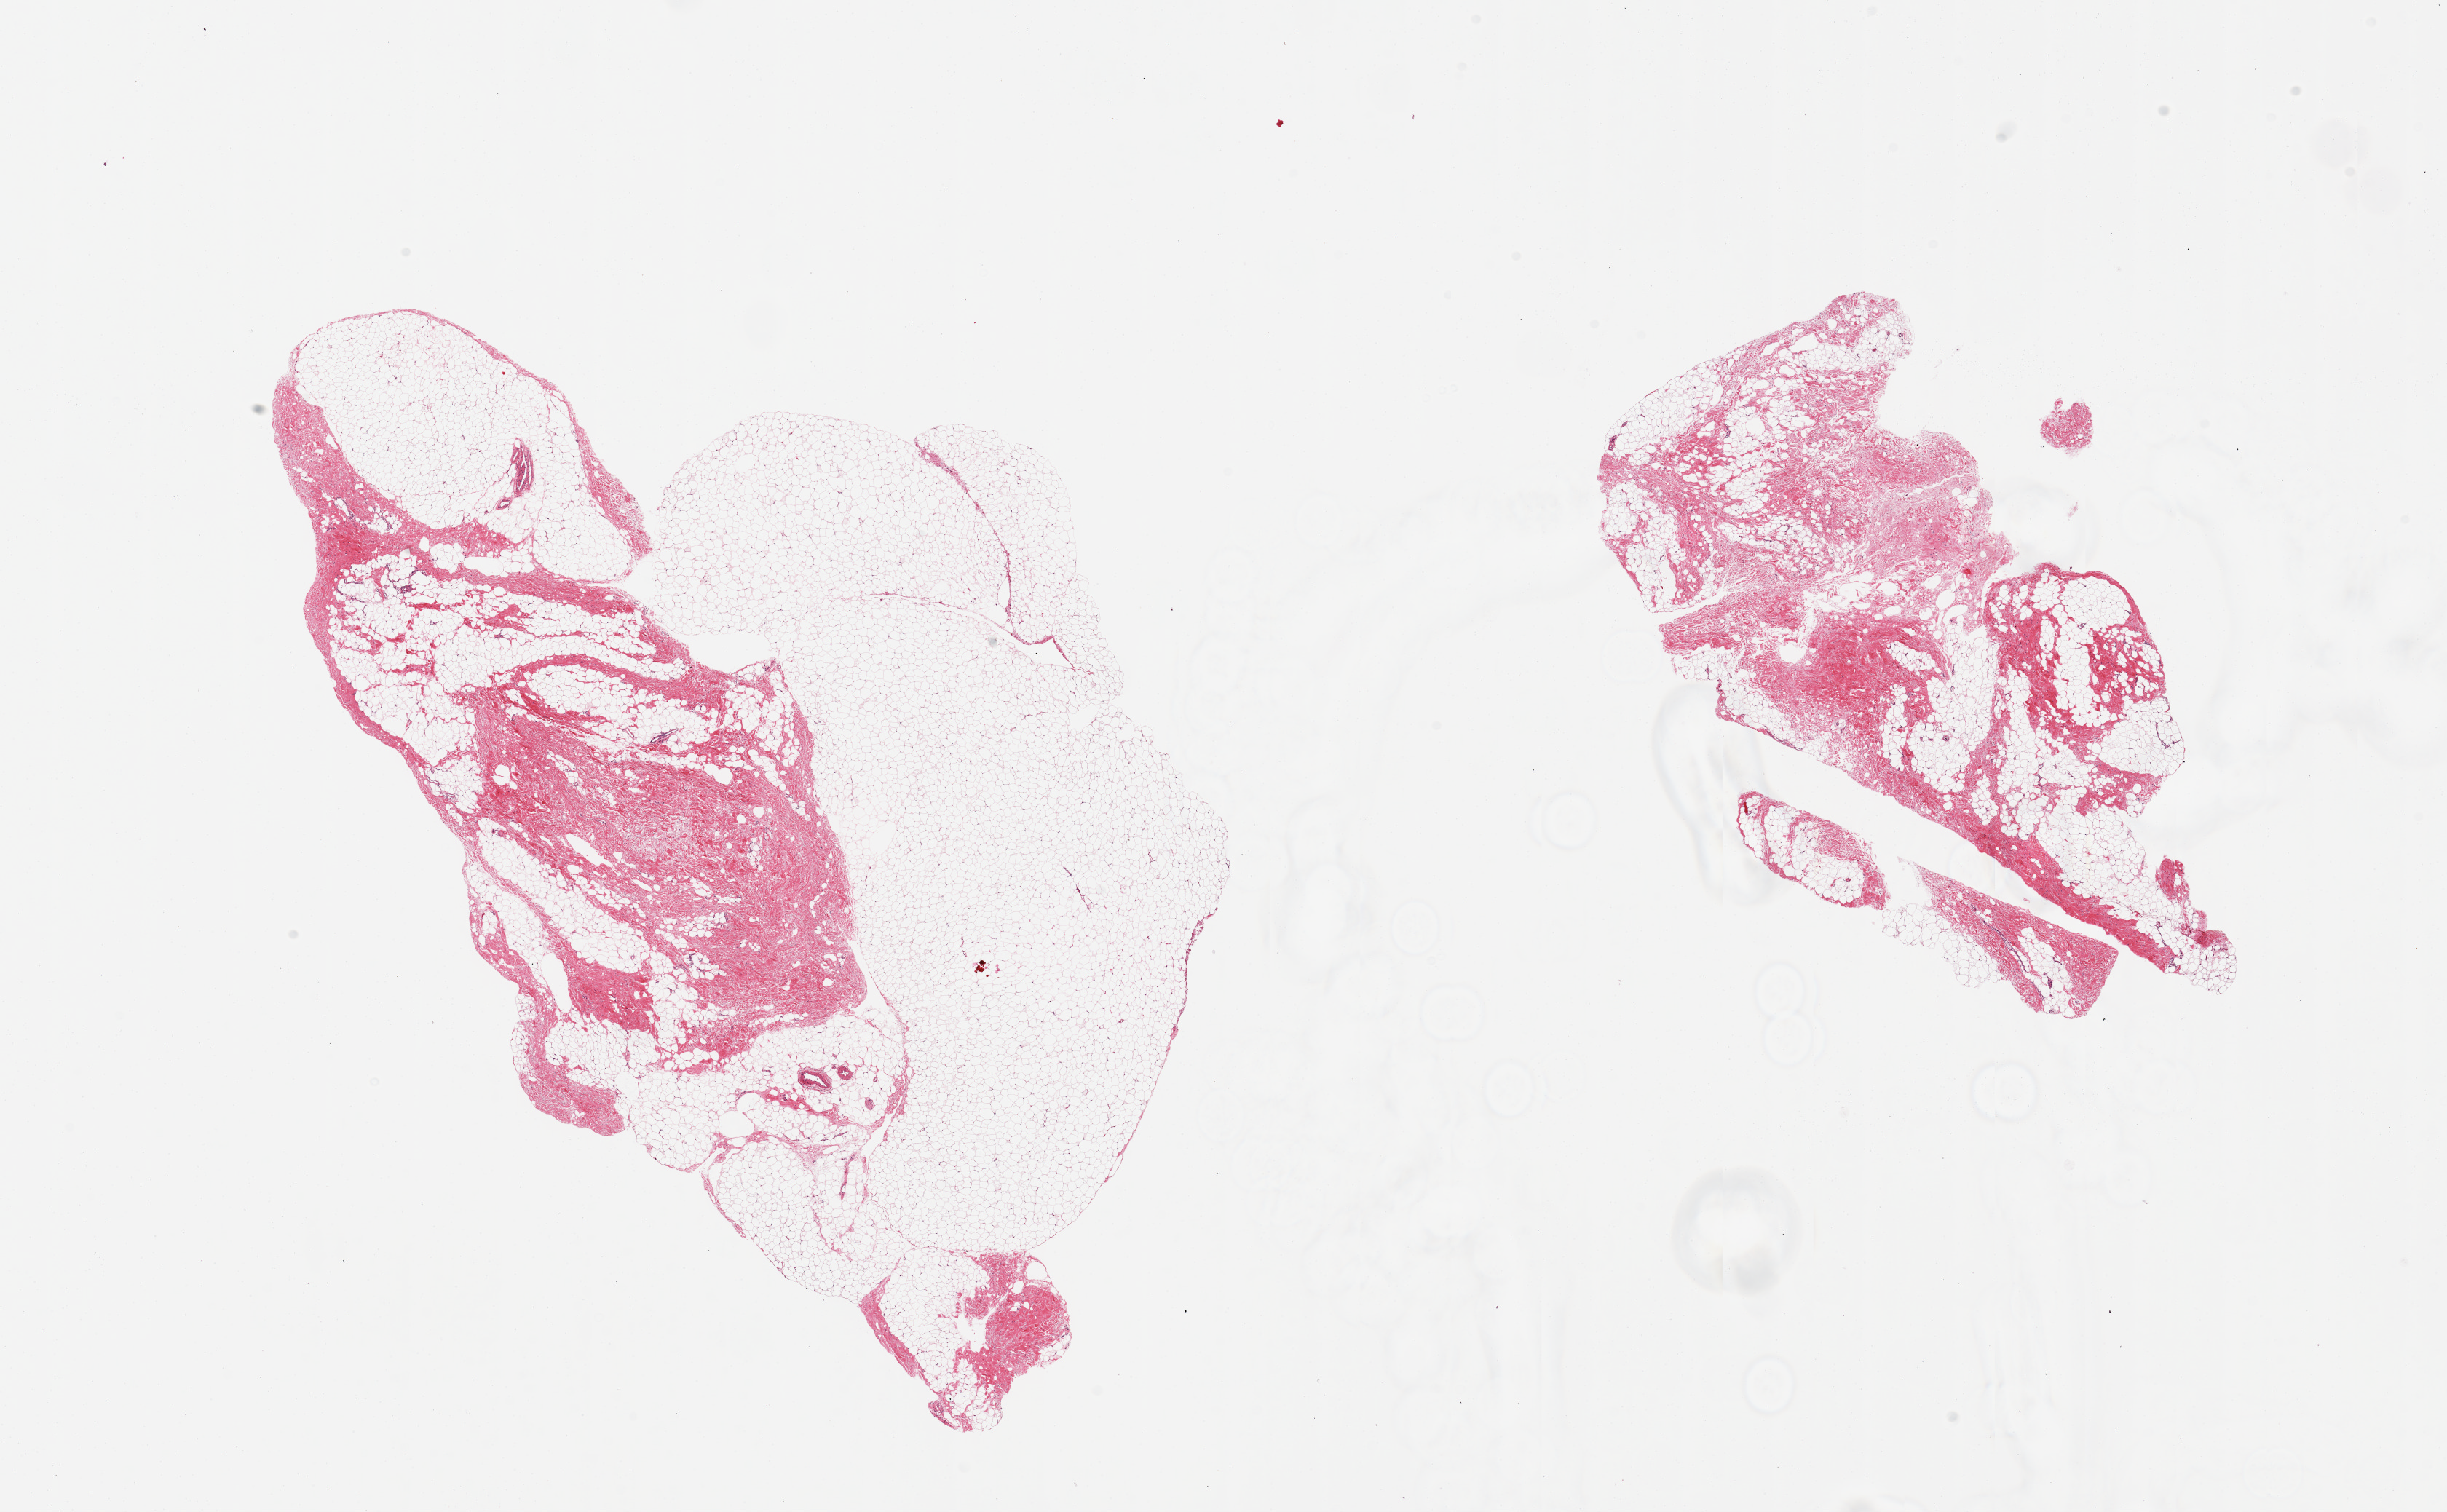
Digitized hematoxylin and eosin (H&E)-stained section, brightfield — a low-resolution overview of the entire scanned area, about 26.6 x 16.4 mm, PAXgene-fixed paraffin-embedded (PFPE) section, target tissue: breast, donor tissue sample.
Pathologist's review note for this sample: 2 pieces; fibrofatty tissue without mammary ducts.